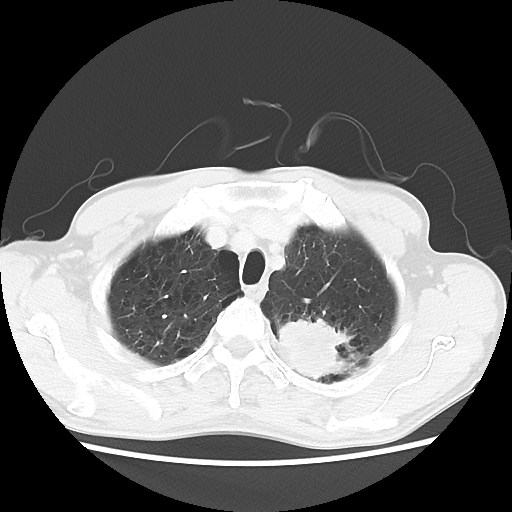
Chest CT, one axial slice; position 54 of 64 along the scan axis; reconstruction kernel LUNG; 120 kVp; lung window (W 1500 / L -600 HU); 512 × 512 image matrix, field of view 346 × 346 mm. Patient: male, 63 years. Case-level facts recorded for this patient, not image findings: clinical TNM (as recorded): T2 N0 M0.
Structures marked on this image (bounding box drawn by a radiologist):
- lung tumour (recorded histology: adenocarcinoma): box from (x=272, y=304) to (x=356, y=385) px